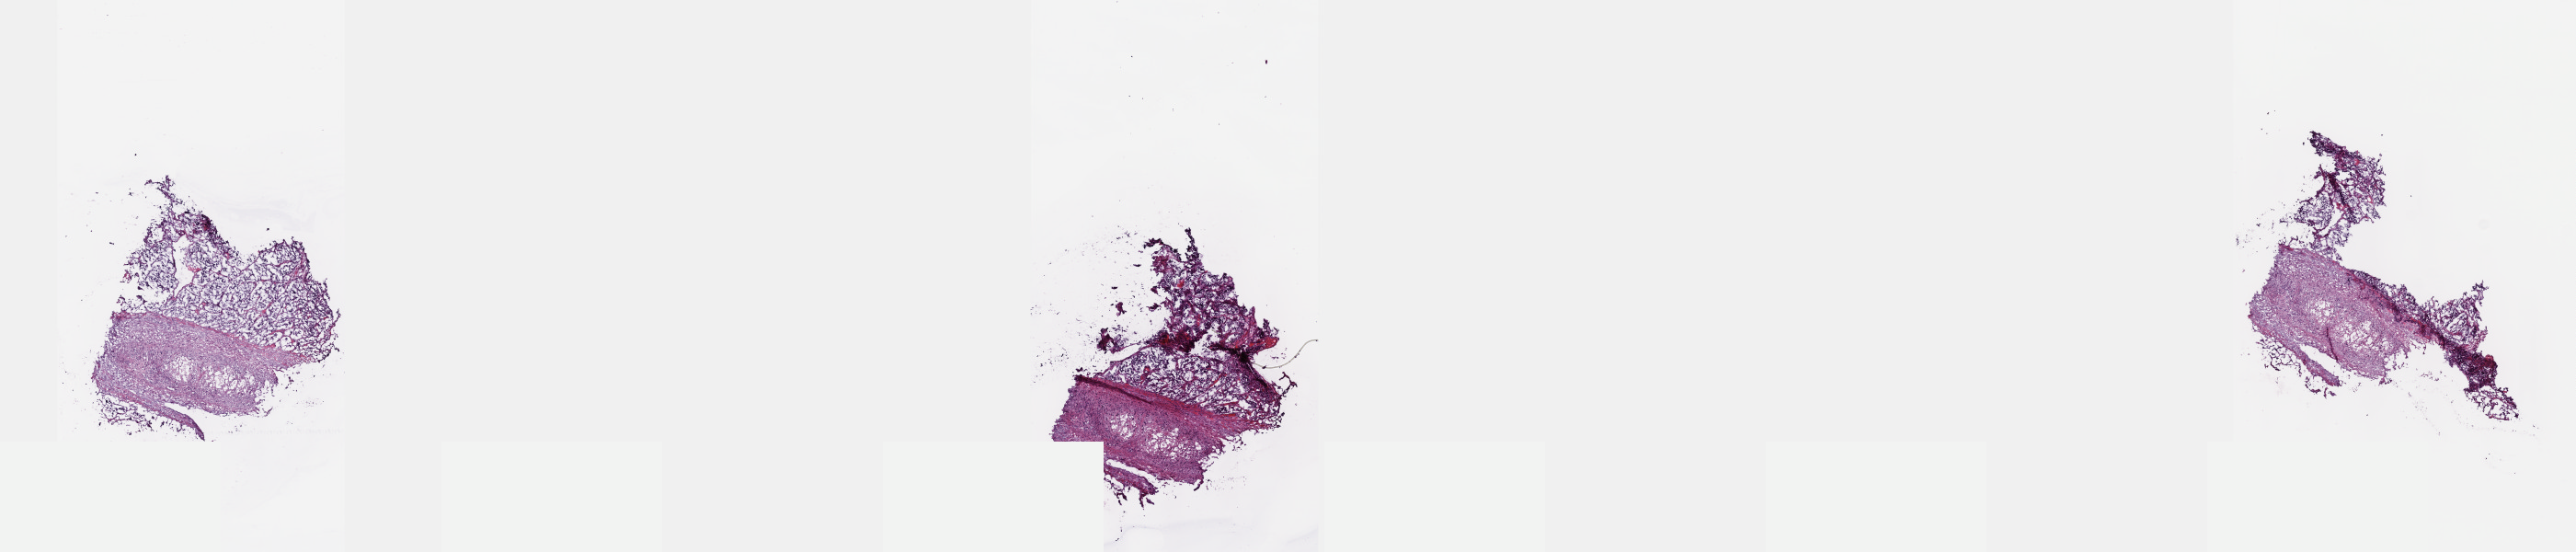
Whole-slide histology image, H&E — whole scanned area (about 22.6 x 4.8 mm) shown as a low-resolution overview. Frozen section from the top of the tissue portion. Retroperitoneum and peritoneum, primary tumour sample. Patient: male, age at initial diagnosis 20 years. Pathologist review of this section (percent, as recorded): tumour cells 80%, tumour nuclei 90%, normal cells 0%, stromal cells 20%, necrosis 0%. Infiltration values recorded for this section: lymphocyte infiltration 0%, monocyte infiltration 0%, neutrophil infiltration 0%.
- histologic diagnosis: Extra-adrenal paraganglioma, malignant (retroperitoneum)